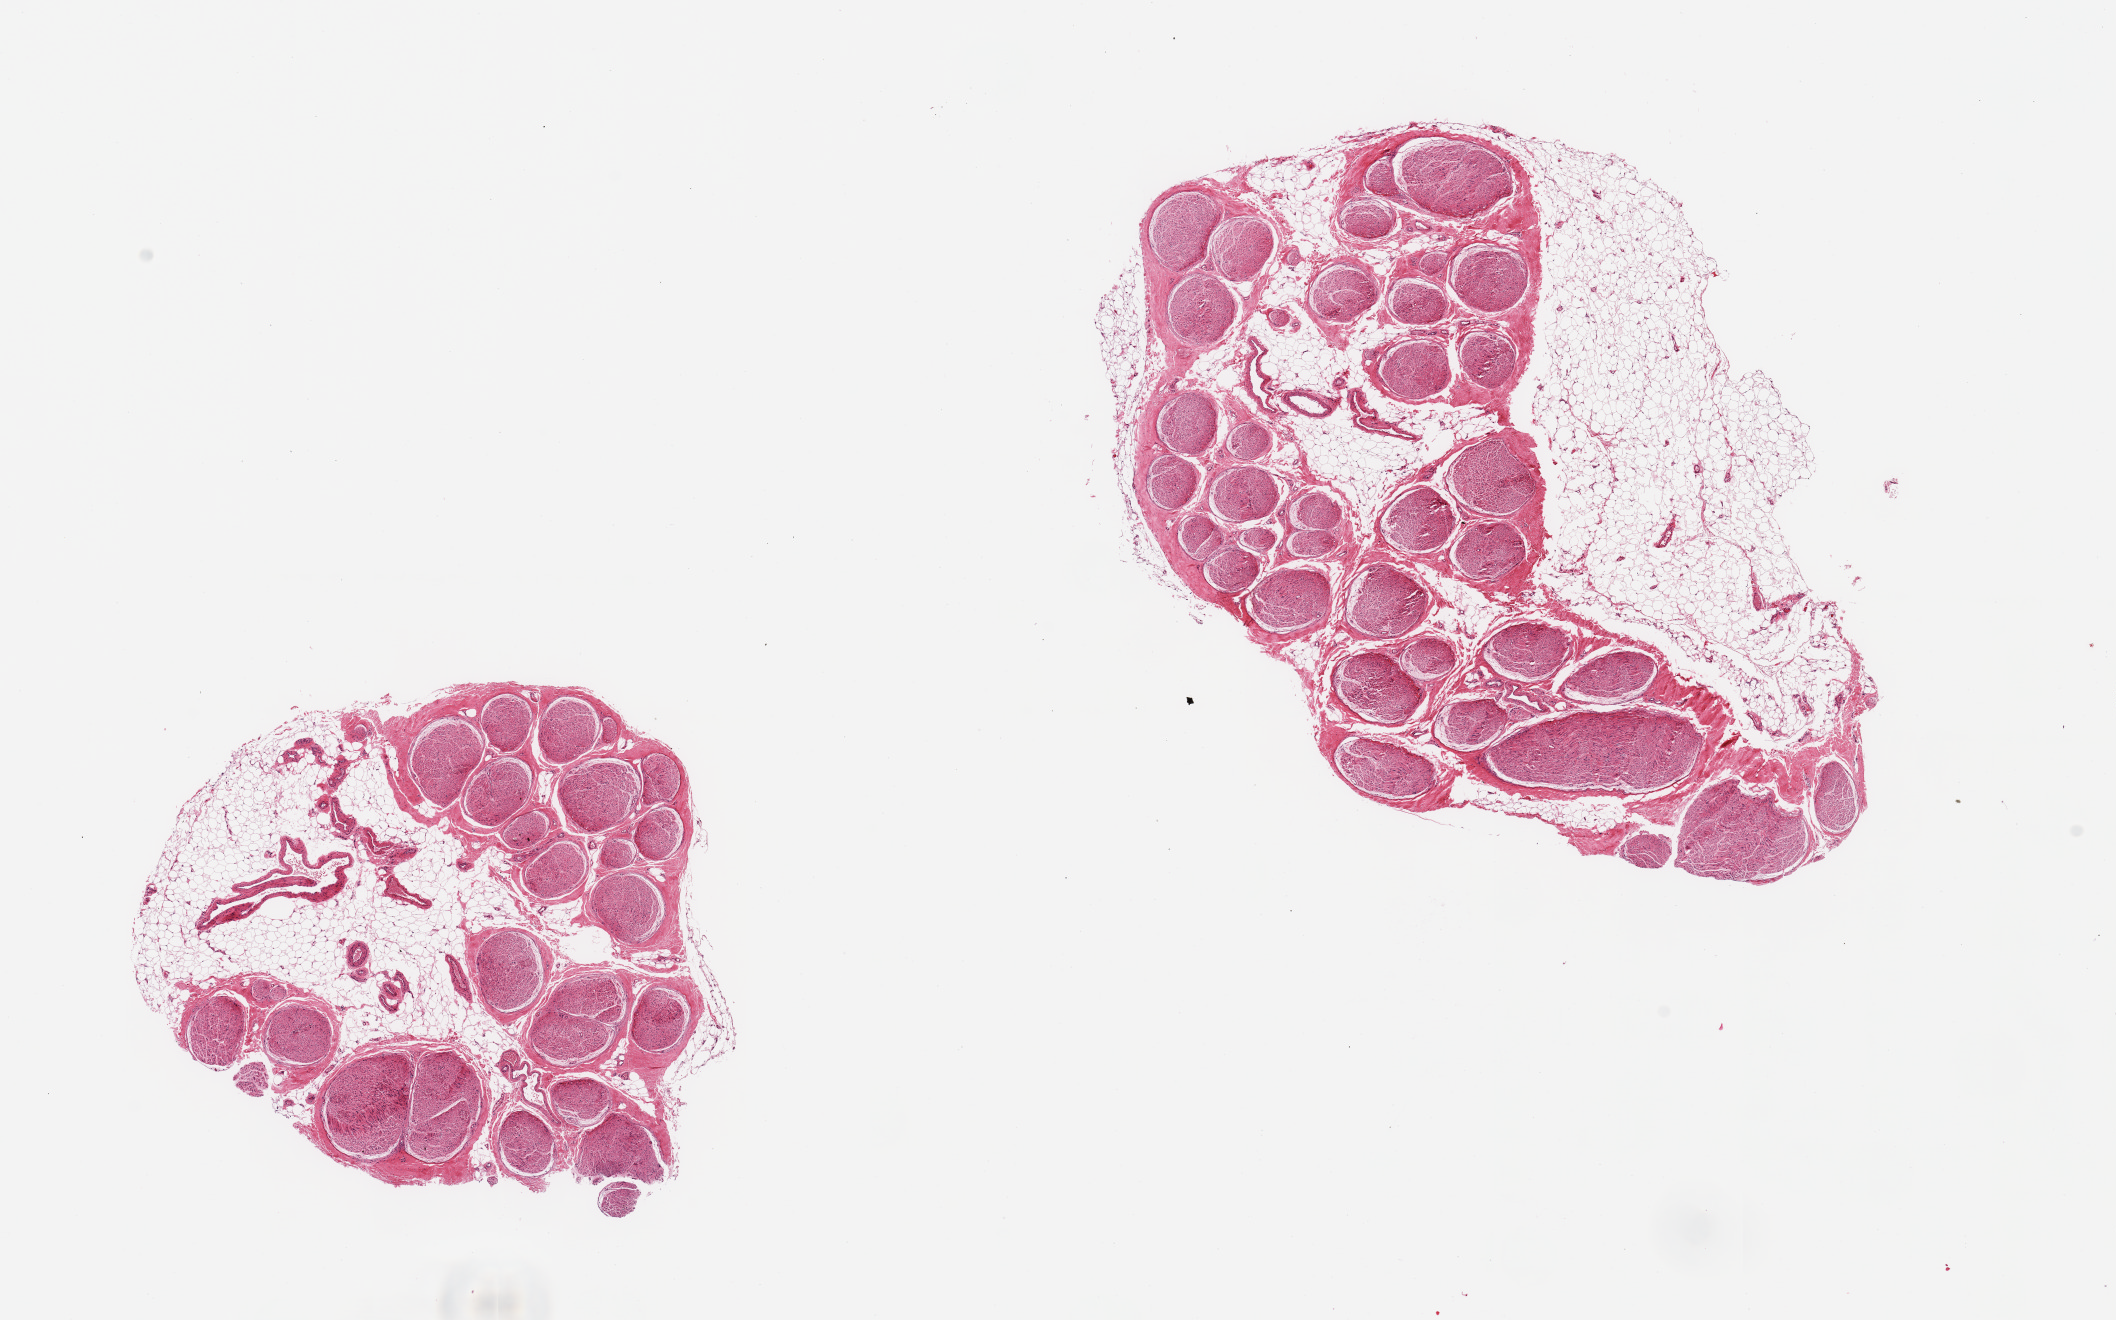
Whole-slide image, hematoxylin and eosin (H&E) stain, low-resolution overview of the scanned area, about 16.7 x 10.4 mm; PAXgene-fixed paraffin-embedded (PFPE) section; sampled site (target tissue): tibial nerve; tissue donor sample. Donor: male.
Pathologist's review note for this sample: 2 pieces; ~40 to 50% attached fat.